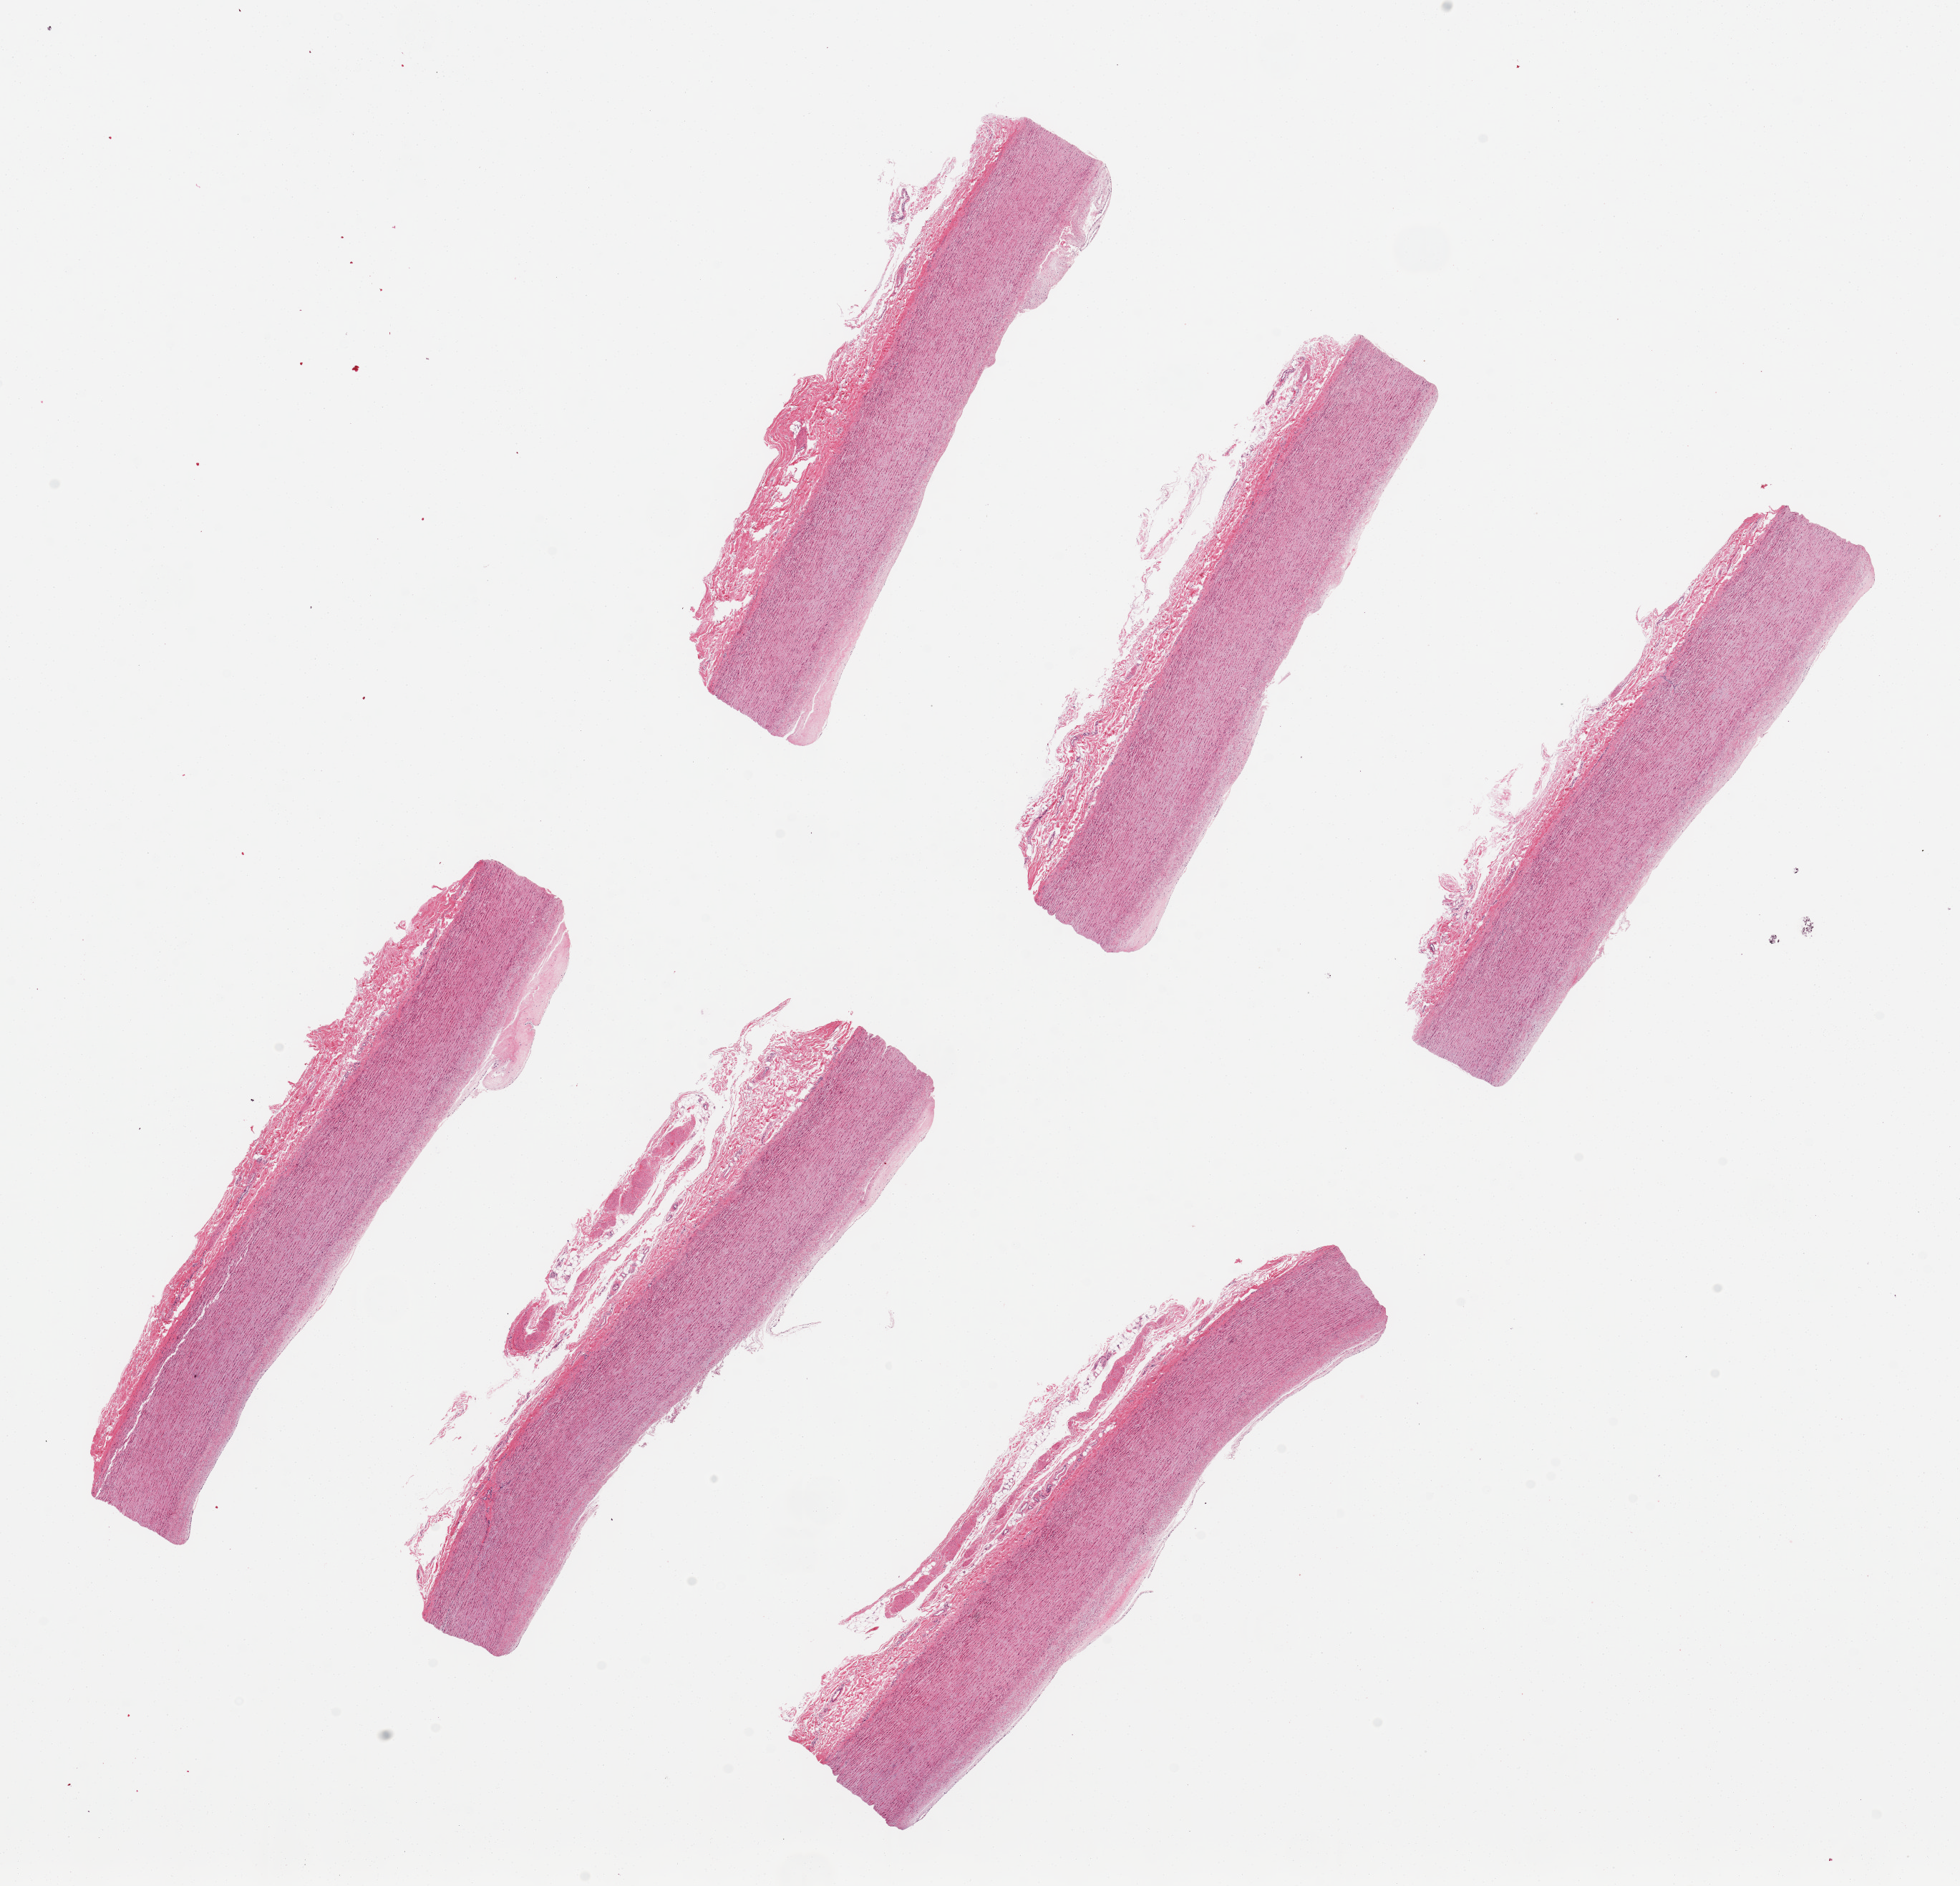
Whole-slide image, haematoxylin and eosin stain, a low-resolution overview of the entire scanned area, about 21.7 x 20.8 mm. PAXgene-fixed, paraffin-embedded tissue. Target tissue: aorta. Donor tissue sample. Donor sex: male.
Reviewer comment on this tissue sample: 6 pieces up to 8x1.6 mm; minimal plaques.